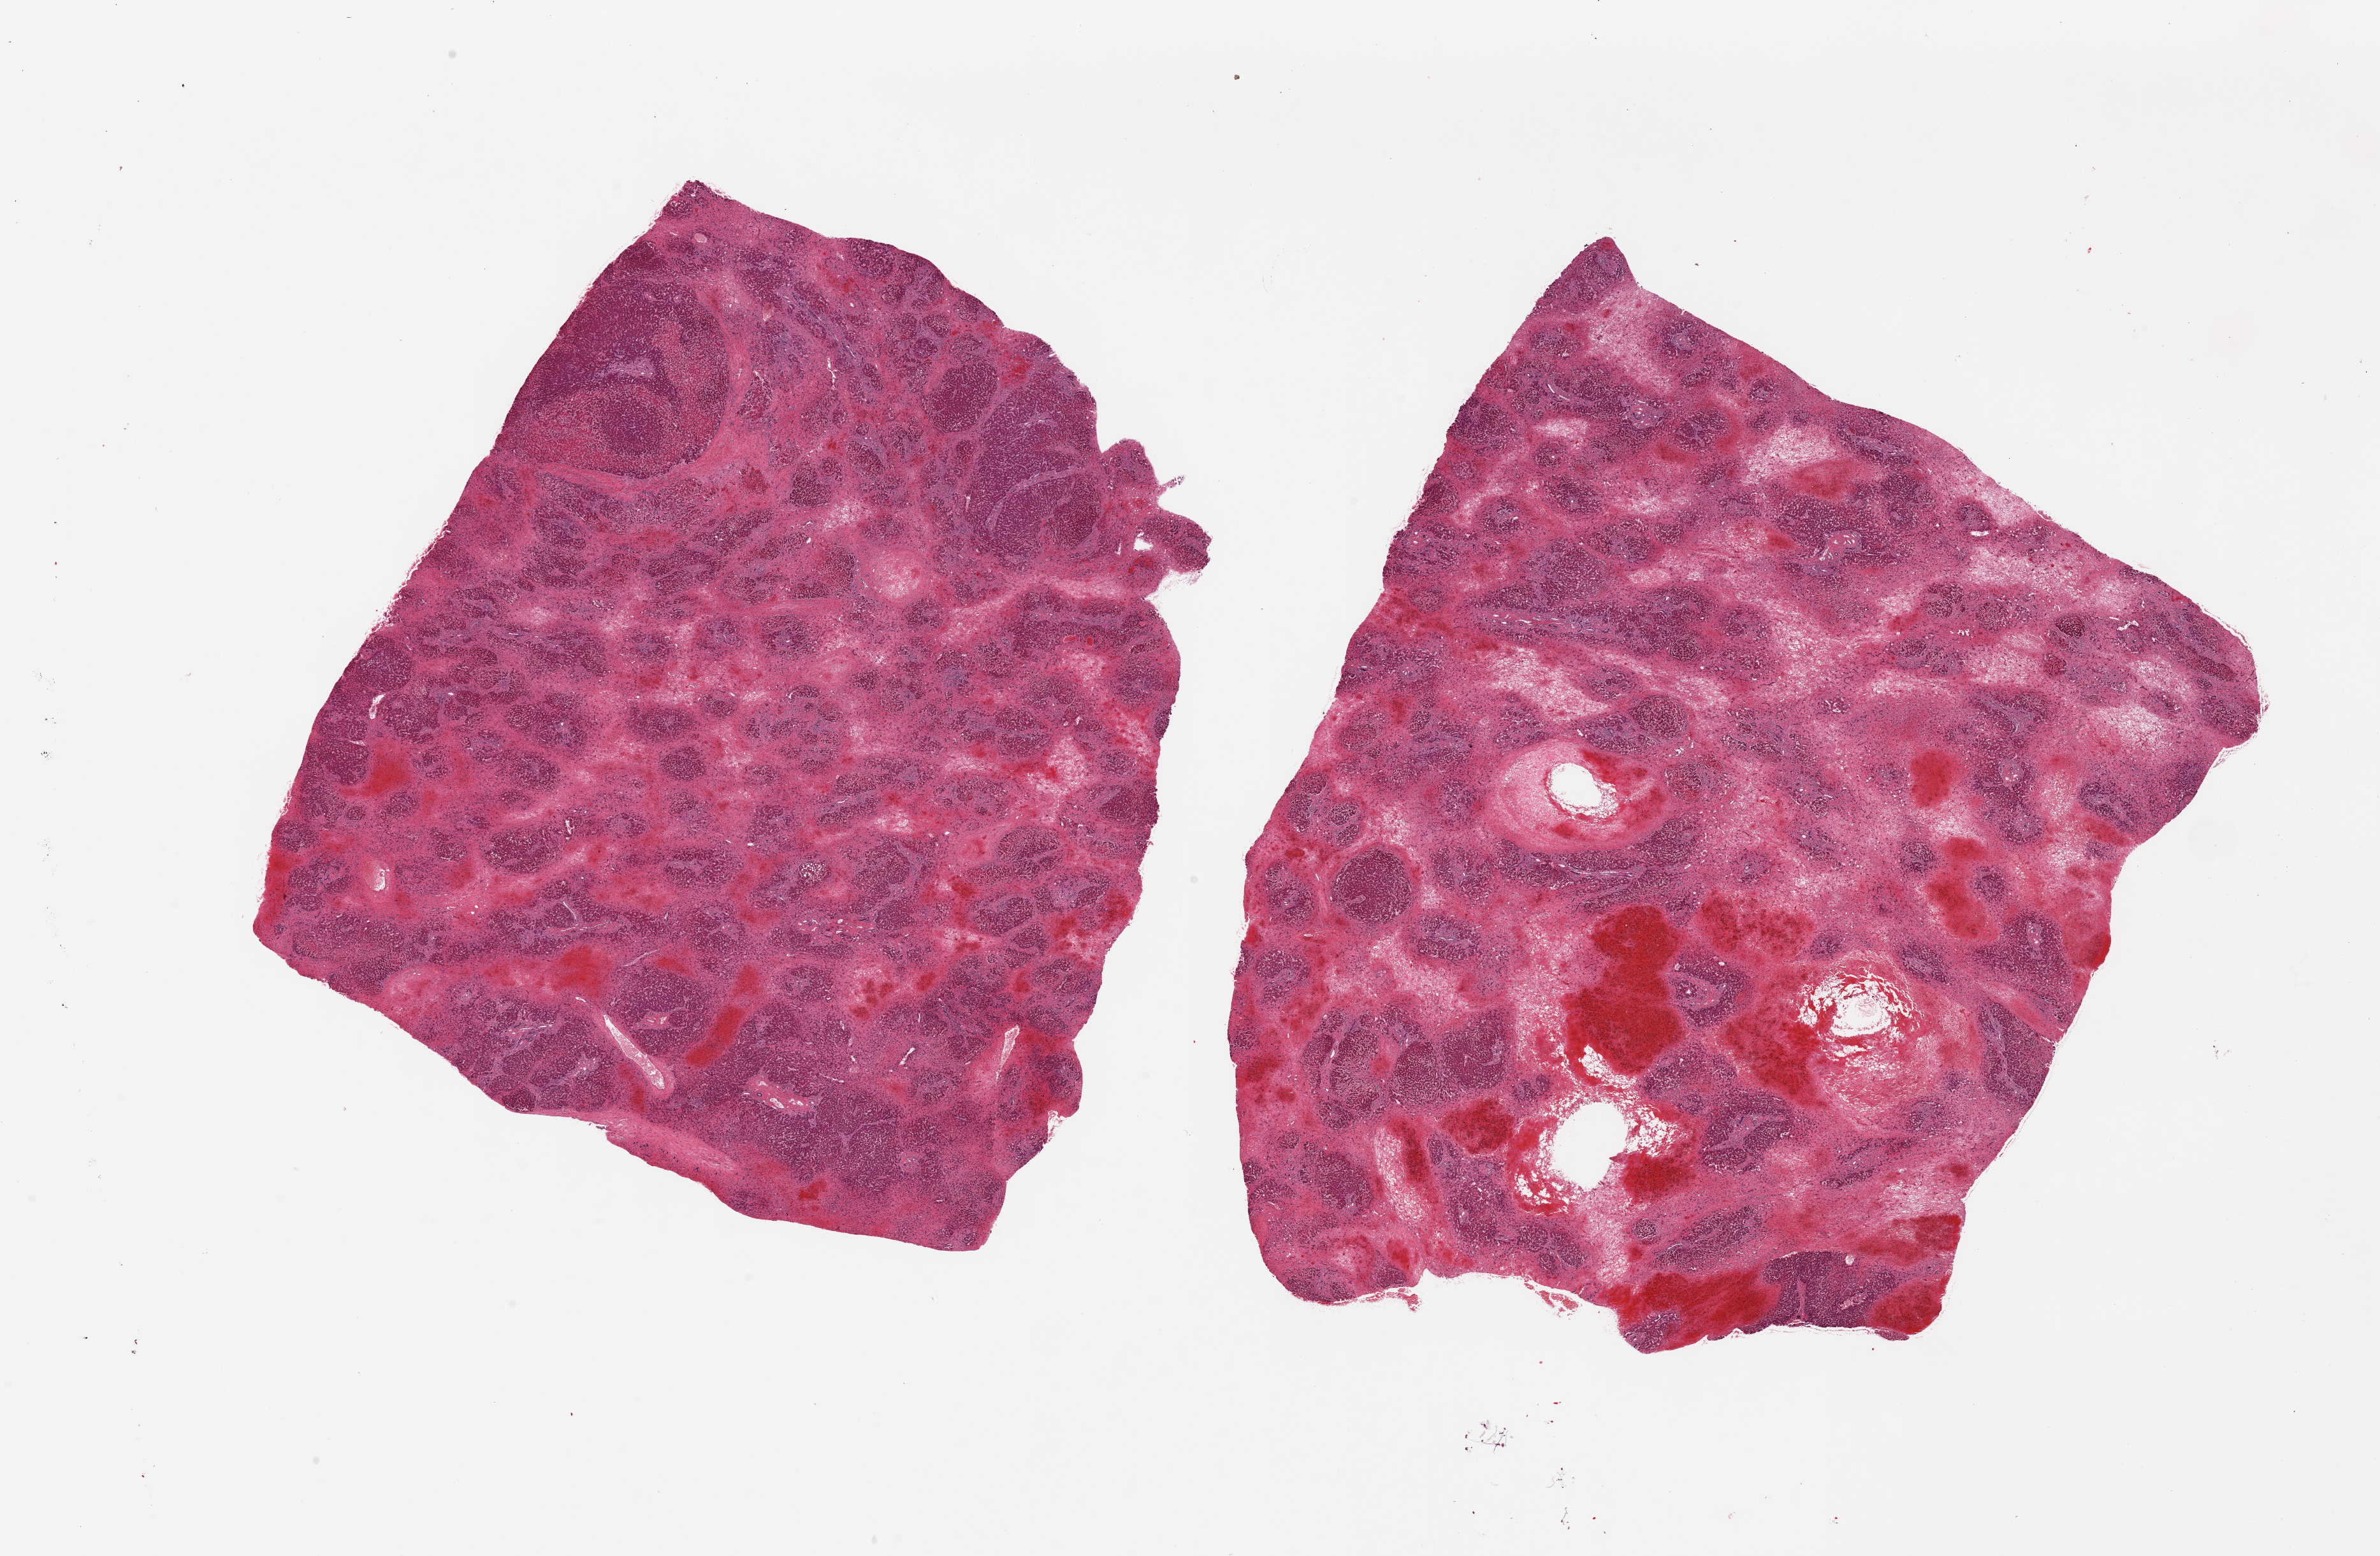
H&E whole-slide image — low-resolution overview of the scanned area, about 29.5 x 19.3 mm; PAXgene-fixed, paraffin-embedded tissue; target tissue: liver; tissue donor sample.
Pathologist's review note for this sample: 2 pieces, extensive congestion, necrosis, 25% of parenchyma preserved.